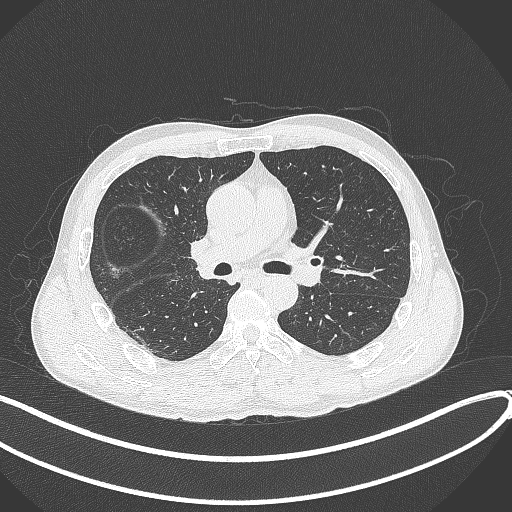
Chest CT, one axial slice. 120 kVp. Lung window (W 1500 / L -600 HU). 1 mm slice thickness. 512 × 512 image matrix, field of view 400 × 400 mm. Male patient, age 53 years. From the clinical record (not read from this slice): clinical TNM (as recorded): T1b N0 M0.
Annotated regions visible in this slice (bounding box drawn by a radiologist):
- lung tumour (recorded histology: squamous cell carcinoma): bounding box (x1, y1, x2, y2) in pixels: (183, 232, 223, 282)